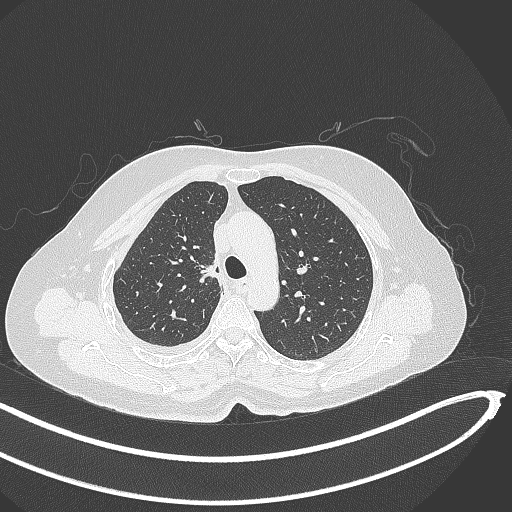
Chest CT, one axial slice; slice 273 of 345 in the series (ordered by position); reconstruction kernel B70f; 120 kVp; lung window (W 1500 / L -600 HU); 1 mm slice thickness; 512 × 512 image matrix. Patient: female, 64 years. From the clinical record (not read from this slice): clinical TNM (as recorded): T1b N0 M1.
Outlined on this slice (rectangle marked by the reading radiologist):
- lung tumour (recorded histology: adenocarcinoma): bounding box (x1, y1, x2, y2) in pixels: (198, 255, 224, 288)